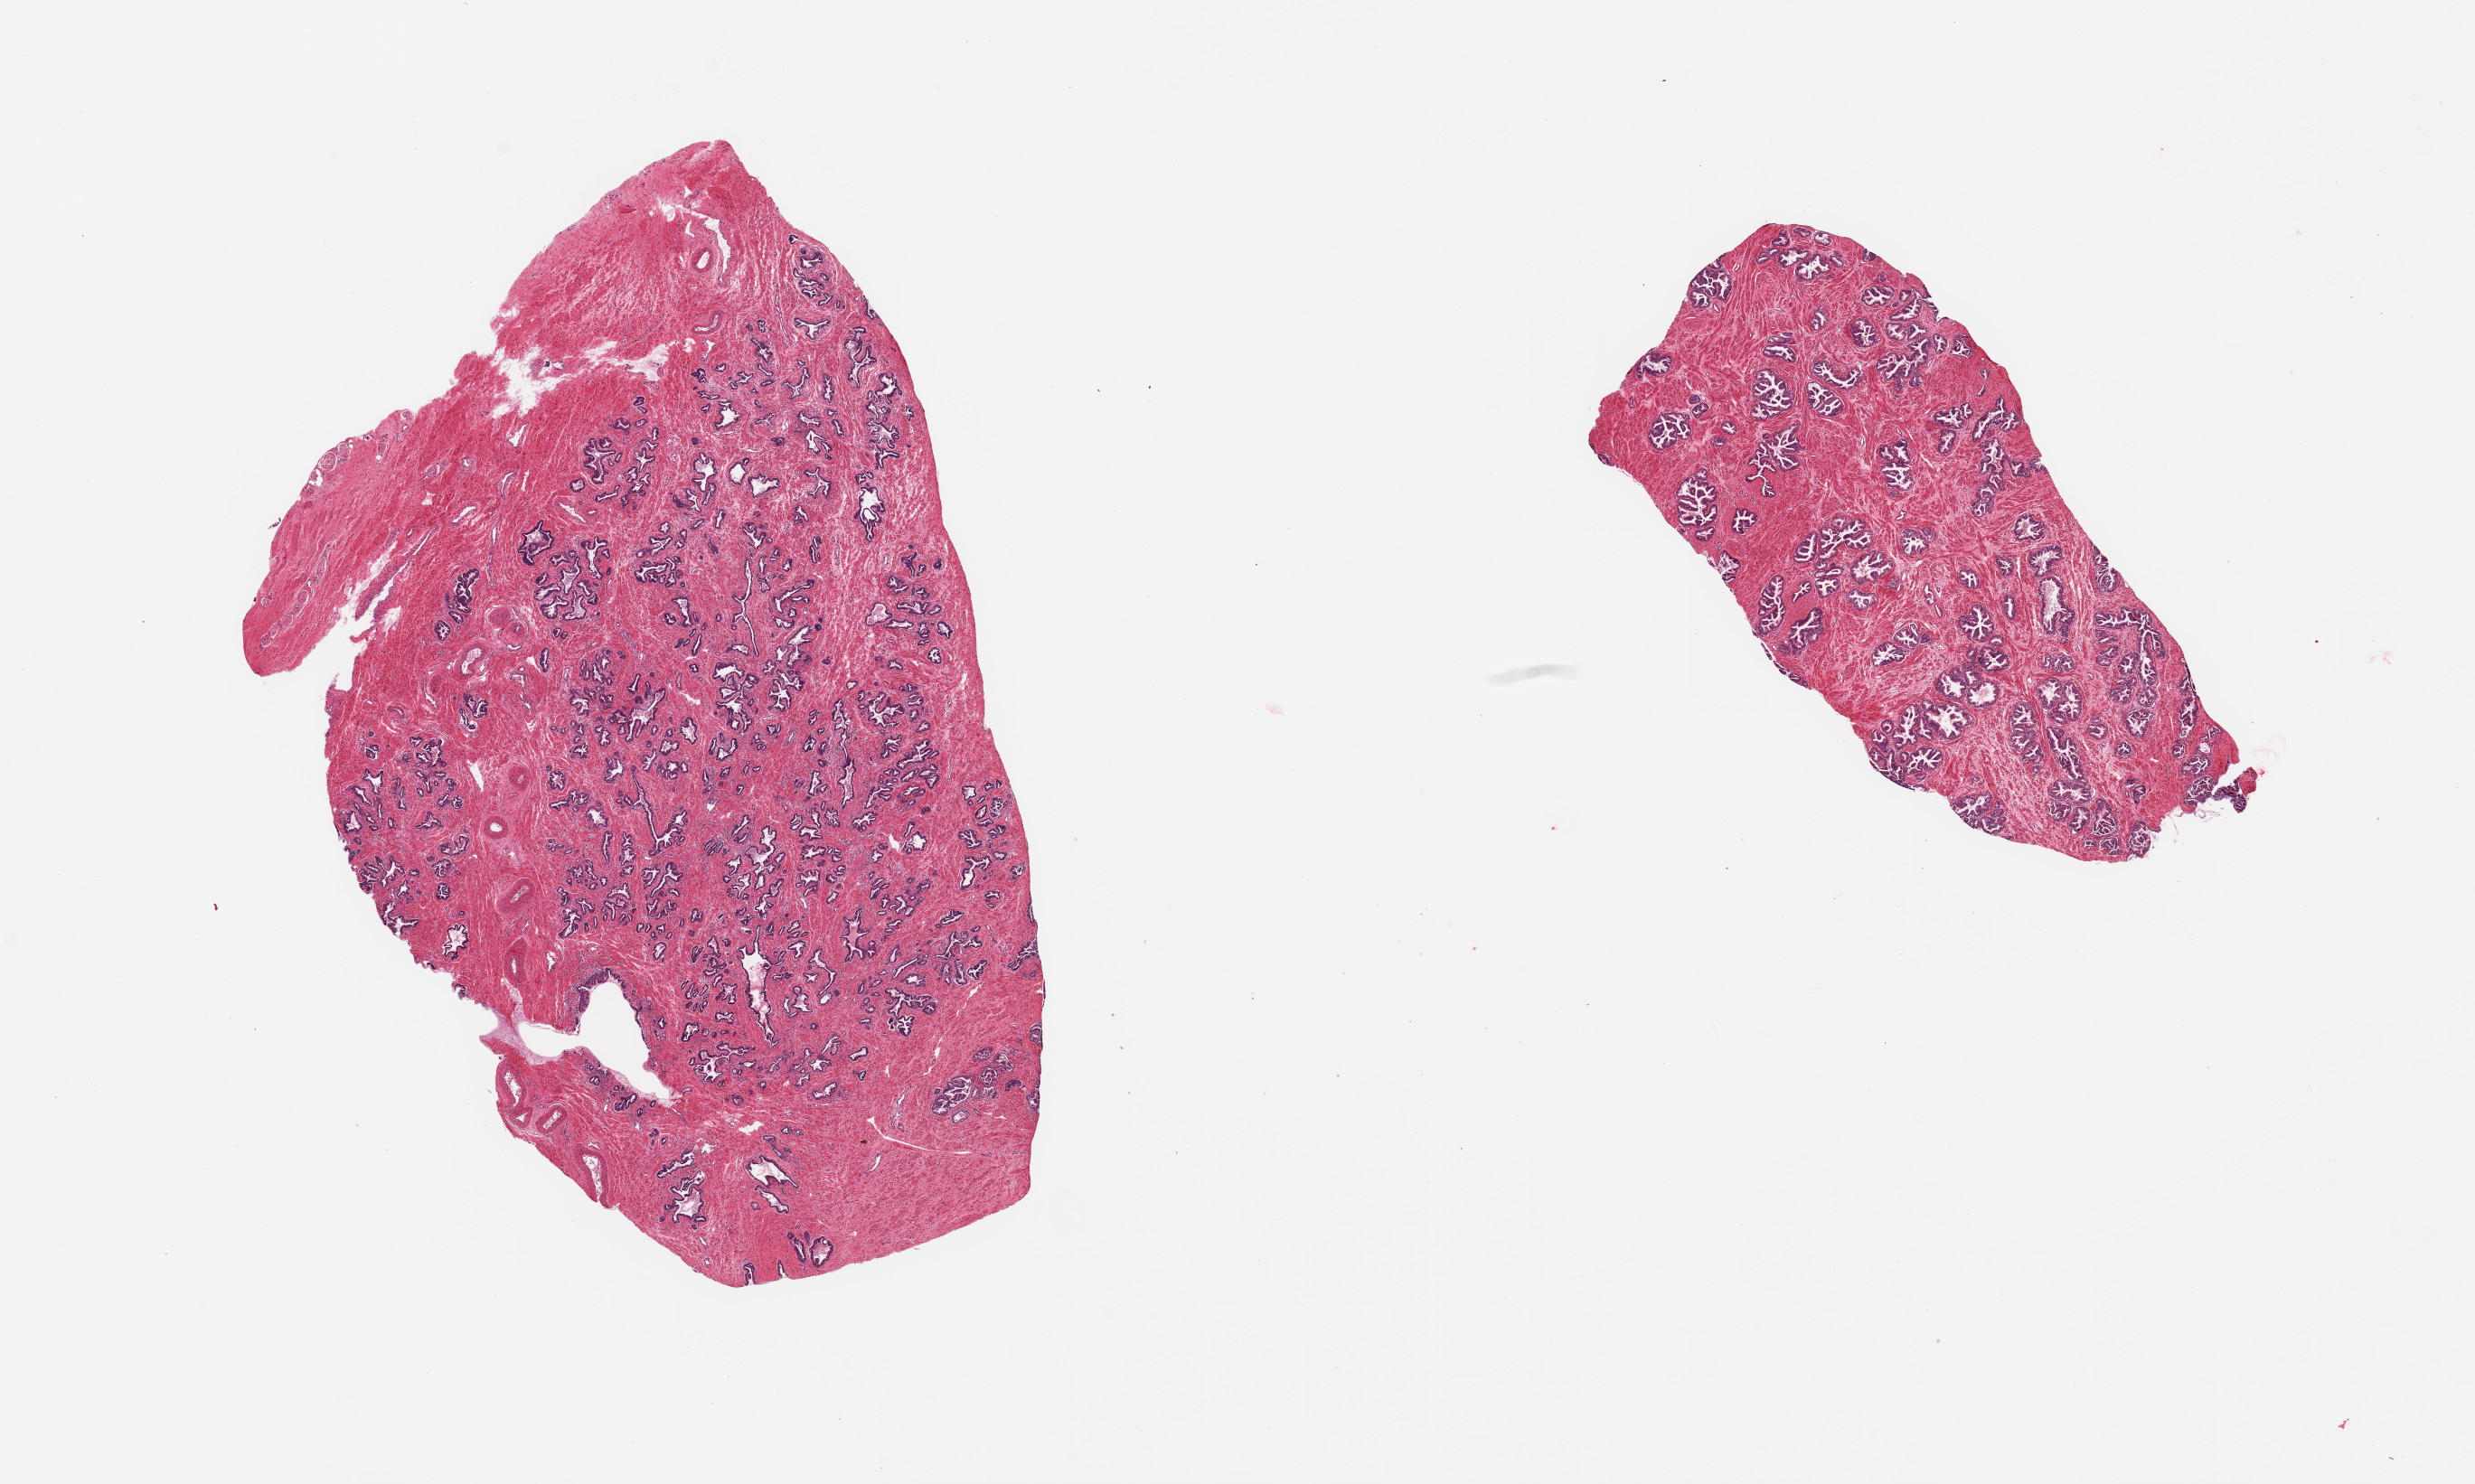
H&E whole-slide image, brightfield — whole scanned area (about 21.7 x 13.0 mm) shown as a low-resolution overview; PAXgene-fixed, paraffin-embedded tissue; sampled site (target tissue): prostate; donor tissue sample. Male donor.
Pathologist's review note for this sample: 2 pieces; well preserved glands without hypertrophy.